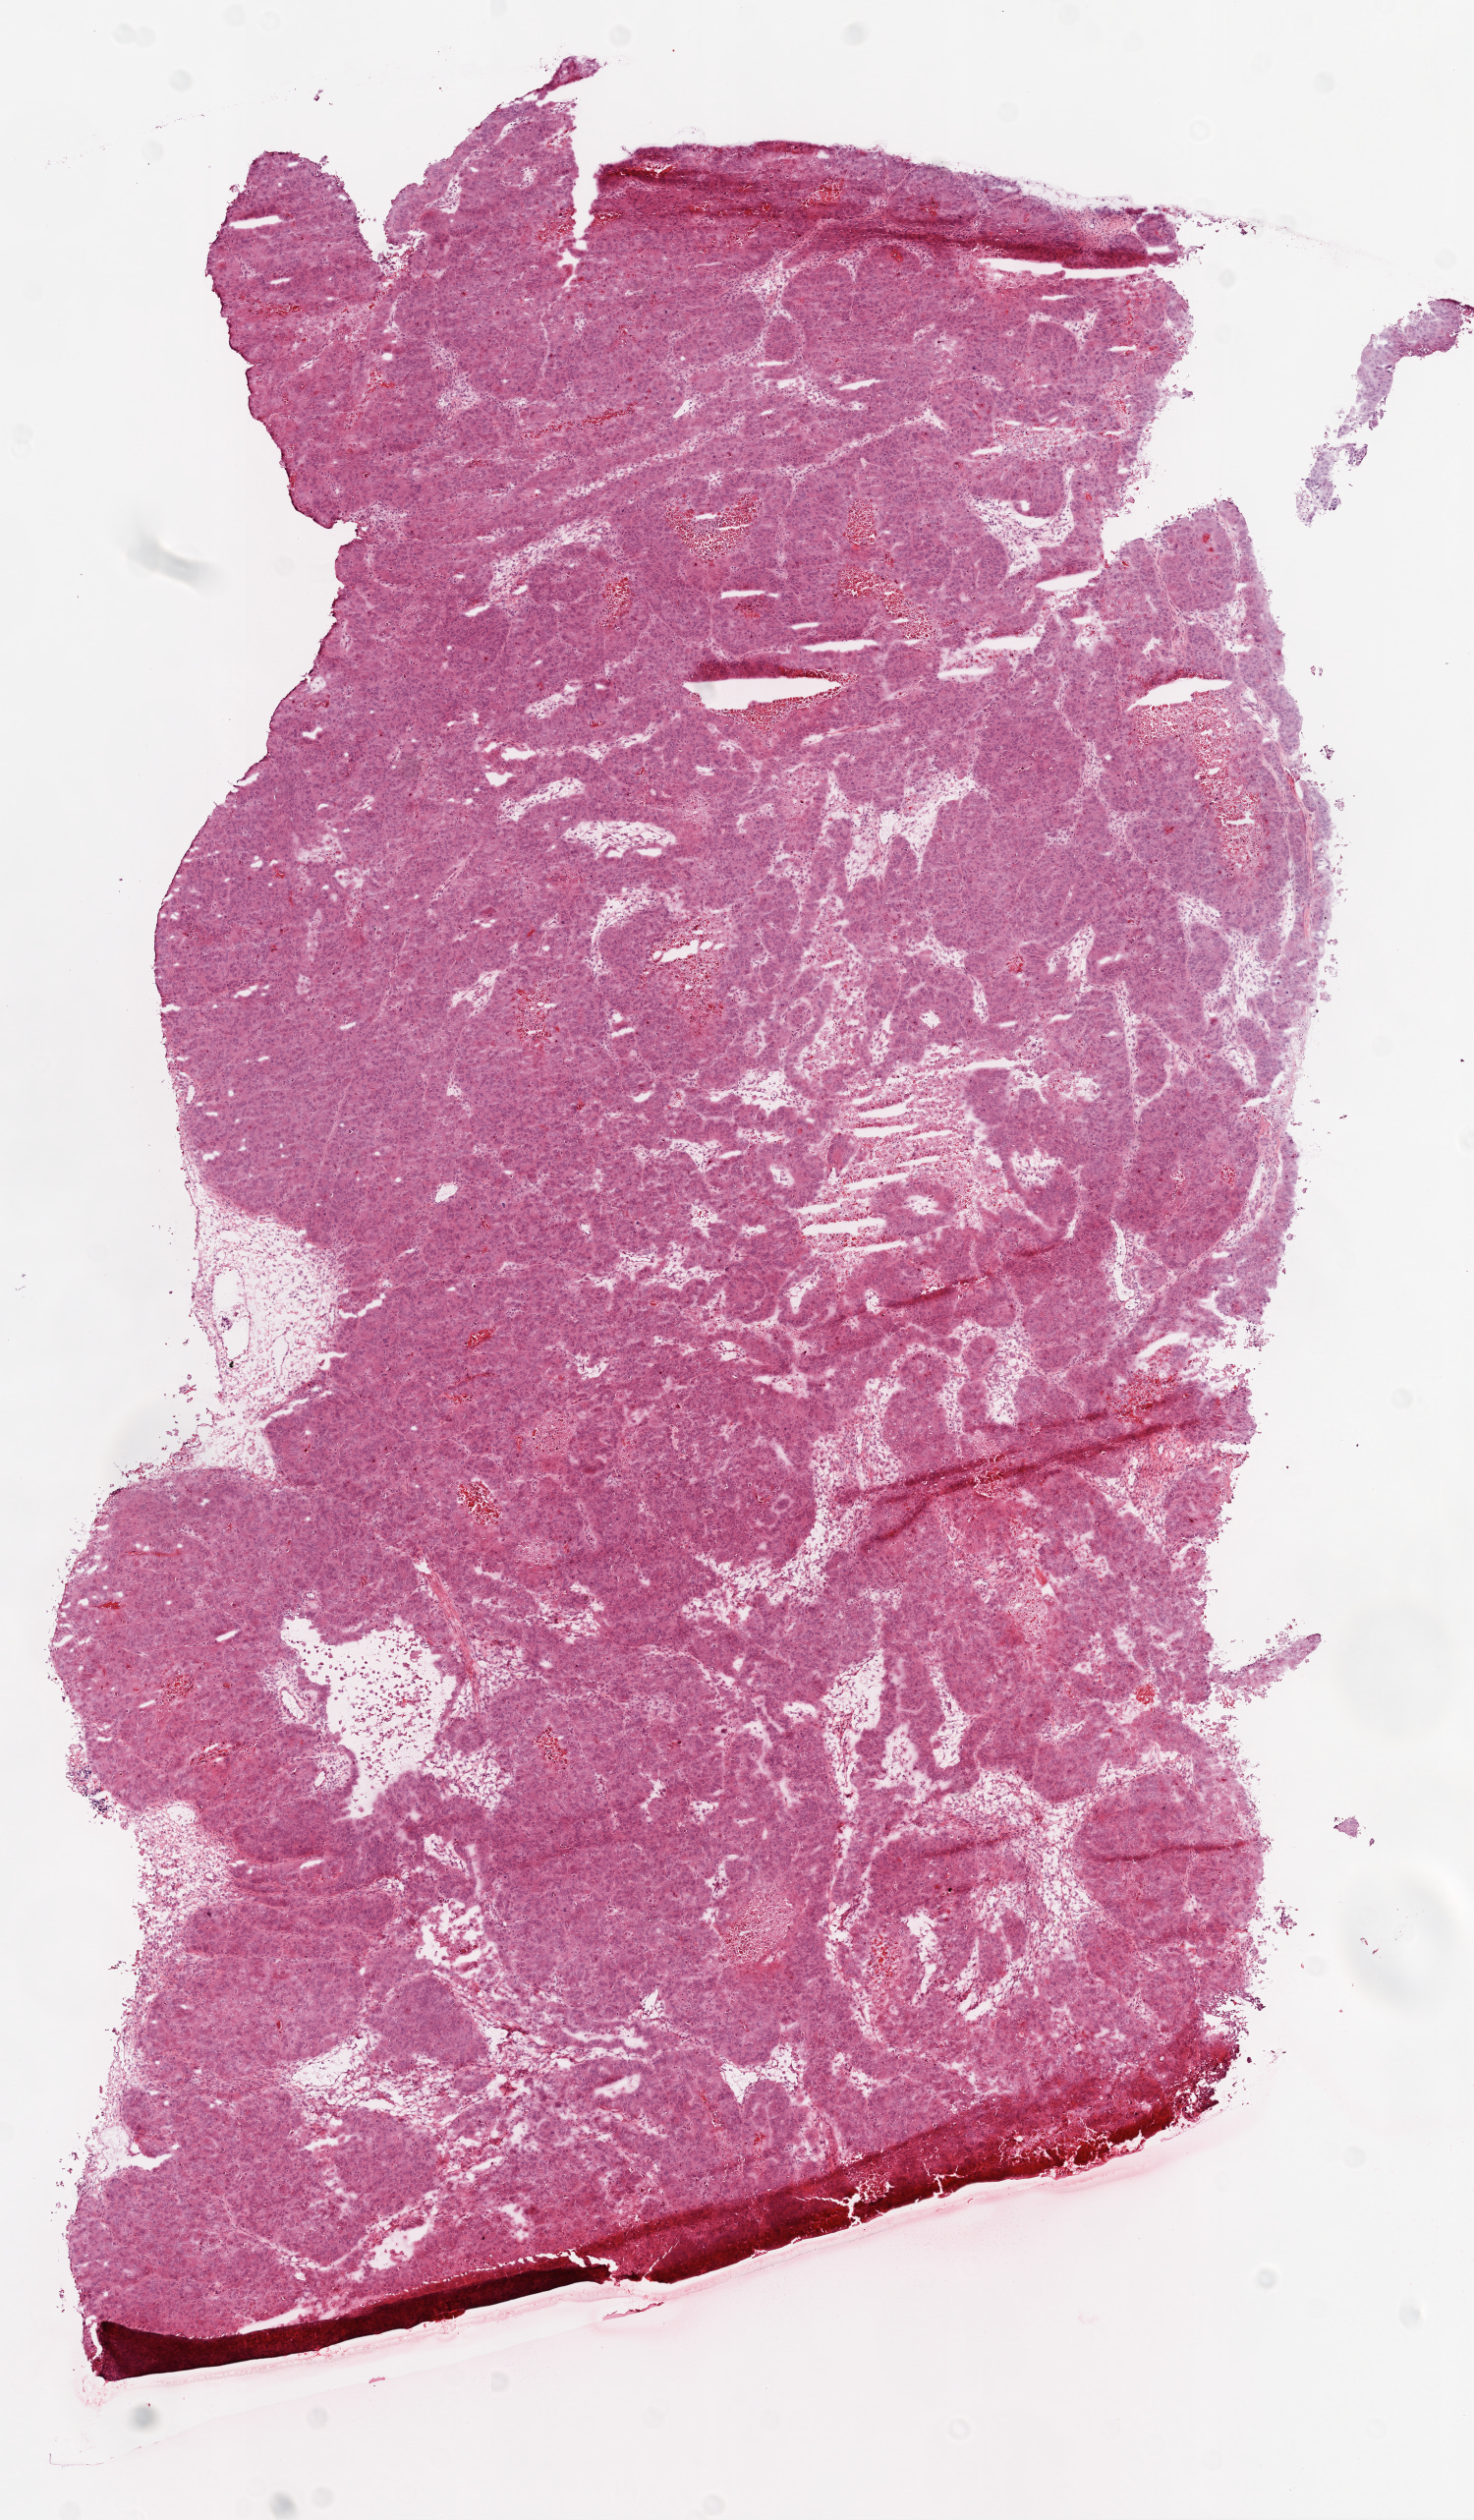
Whole-slide histology image, Hematoxylin and eosin (H&E) stained, a low-resolution overview of the entire scanned area, about 6.0 x 10.3 mm. Frozen section from the top of the tissue portion. Primary tumour sample from the ovary. Patient: female, age at initial diagnosis 43 years. Histologic grade: G3 (poorly differentiated). Composition of this section per pathologist review: tumour cells 85%, tumour nuclei 90%, normal cells 0%, stromal cells 10%, necrosis 5%. Inflammatory infiltration, as recorded: lymphocyte infiltration 1%.
• histologic diagnosis: Serous cystadenocarcinoma, NOS
• FIGO stage: IIIC